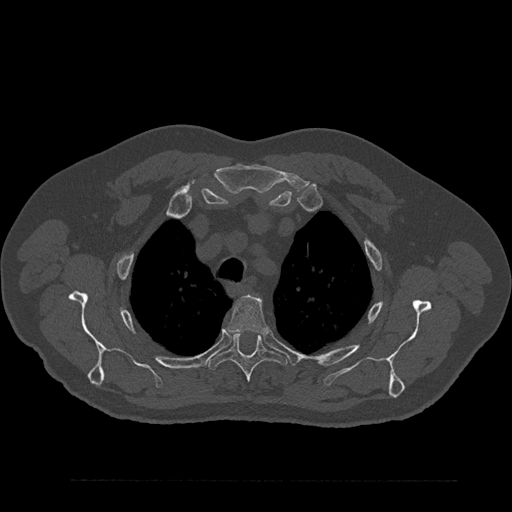
CT including the spine, one axial slice. Position 659 of 797 along the scan axis. 120 kVp. Bone window (W 1800 / L 400 HU). 0.5 mm slice thickness. 512 × 512 image matrix, field of view 430 × 430 mm. Male patient, age 61 years. Case-level facts recorded for this patient, not image findings: primary cancer: prostate.
Structures marked on this image (semi-automatic segmentation, software-assisted and operator-edited):
- T3 vertebra: bounding box [x1, y1, x2, y2] px = [228, 295, 266, 334]
- T4 vertebra: [207, 332, 287, 382]